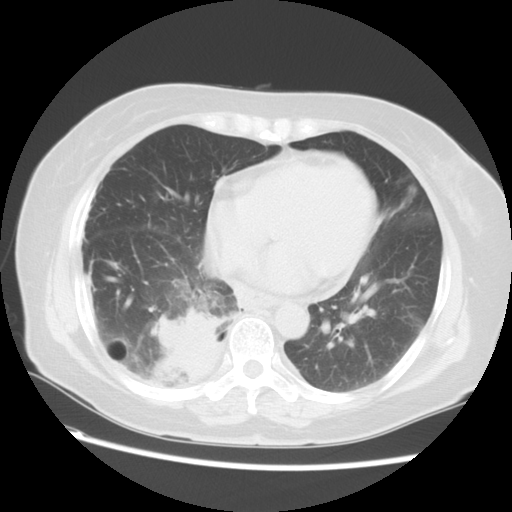
Chest CT, one axial slice. Position 25 of 57 along the scan axis. Reconstruction kernel STANDARD. 120 kVp. Lung window (W 1500 / L -600 HU). 5 mm slice thickness. 512 × 512 image matrix, field of view 350 × 350 mm. Female patient, age 69 years. From the clinical record (not read from this slice): clinical TNM (as recorded): T2 N1 M1a.
Structures marked on this image (rectangle marked by the reading radiologist):
- lung tumour (recorded histology: adenocarcinoma): bounding box [x1, y1, x2, y2] px = [148, 299, 223, 400]